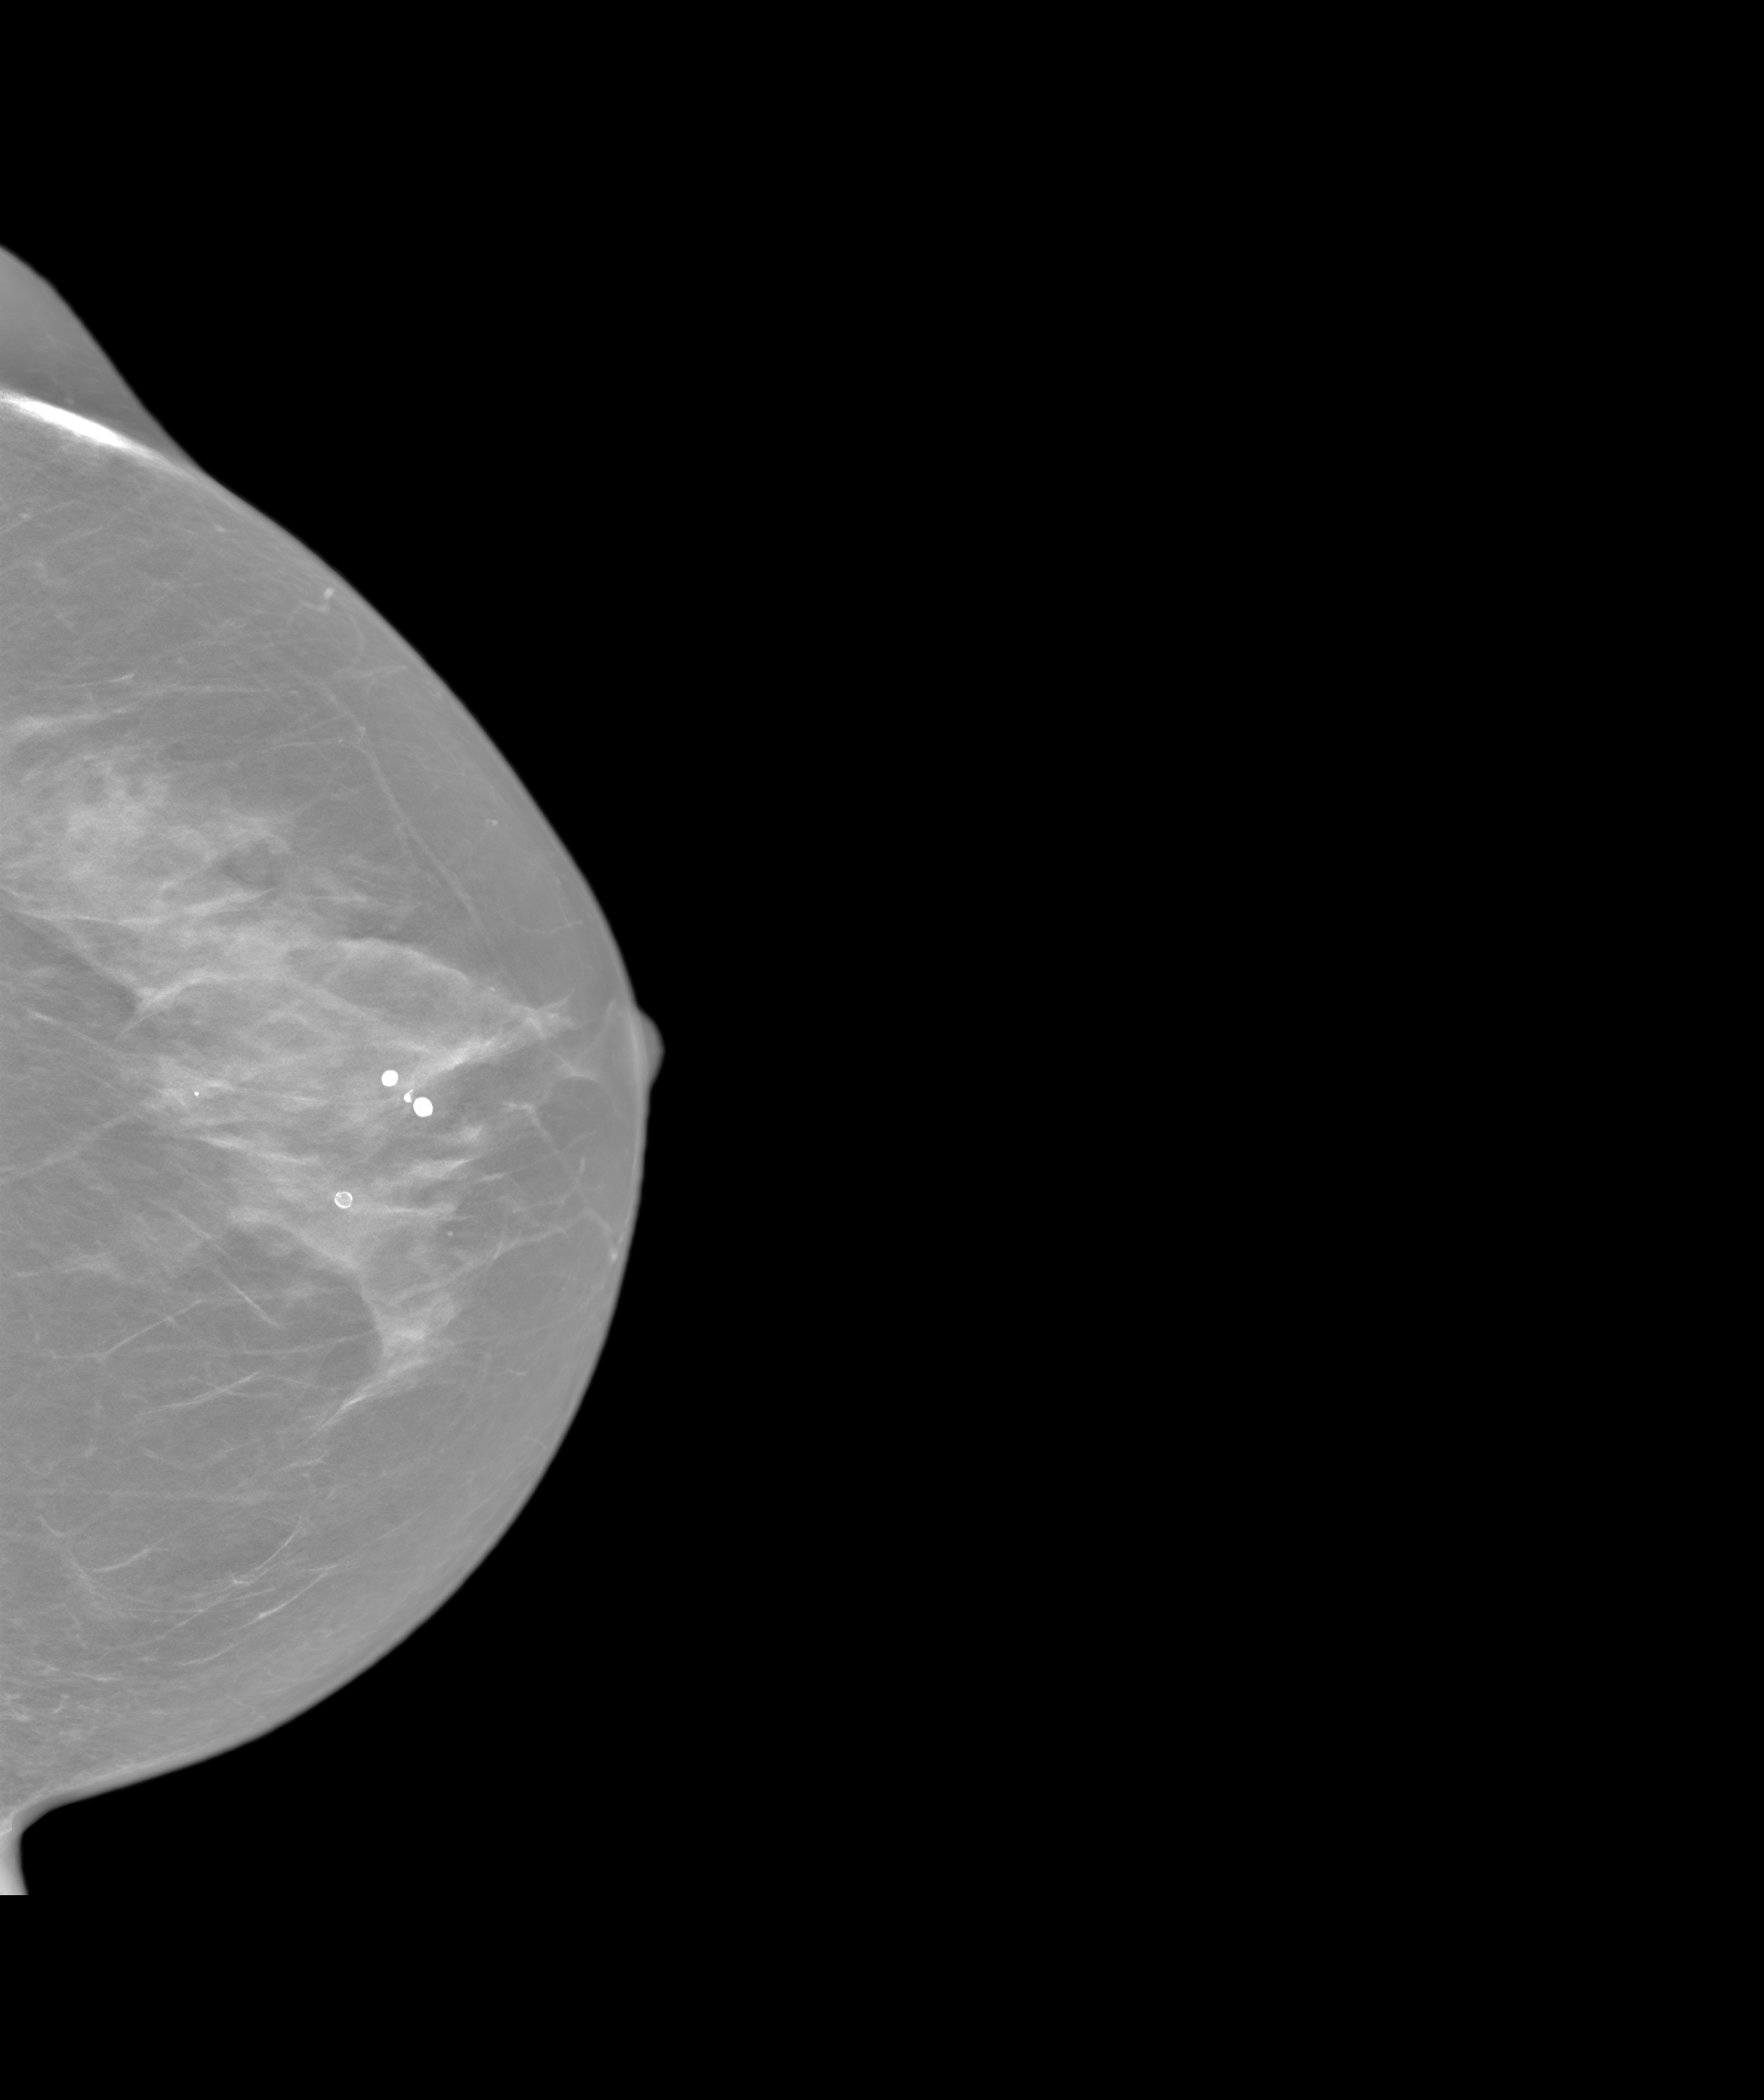
Annual screening mammography examination.
Image type: synthesized 2-D view from tomosynthesis. Breast: left. Projection: craniocaudal (CC) view.